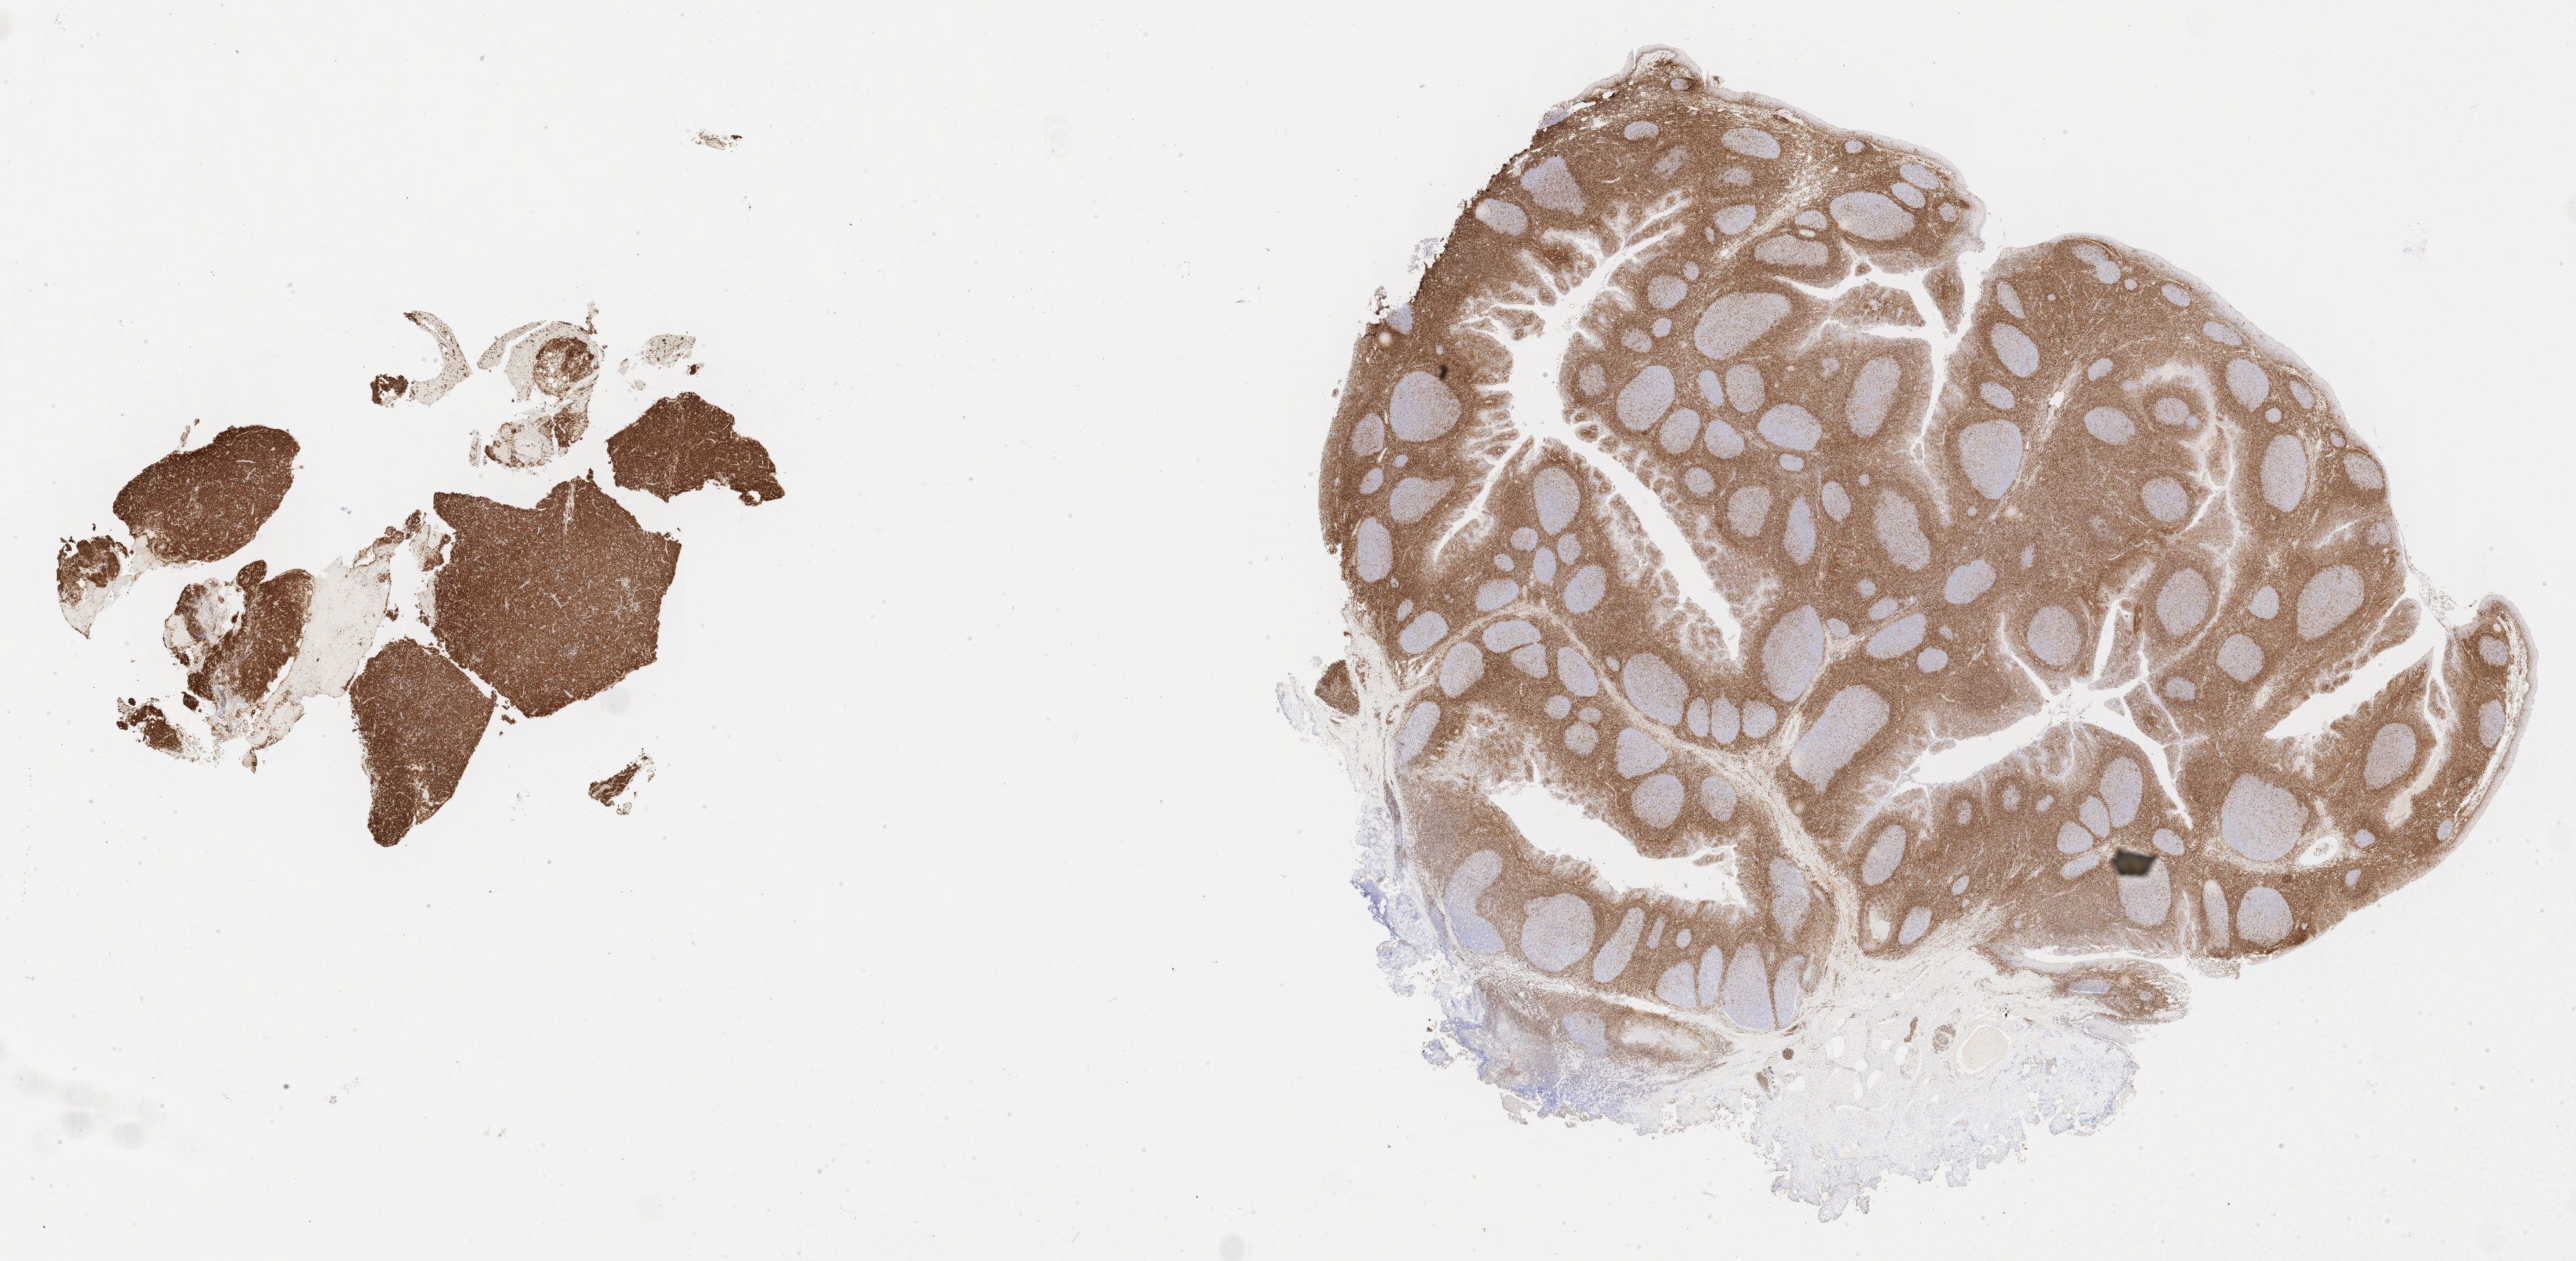
IHC for BCL2, whole-slide image, a low-resolution overview of the entire scanned area, about 32.2 x 15.8 mm; tumor tissue; anatomic site: lymph node. Patient female; aged 71.
Histologic diagnosis: Diffuse large B-cell lymphoma, NOS.